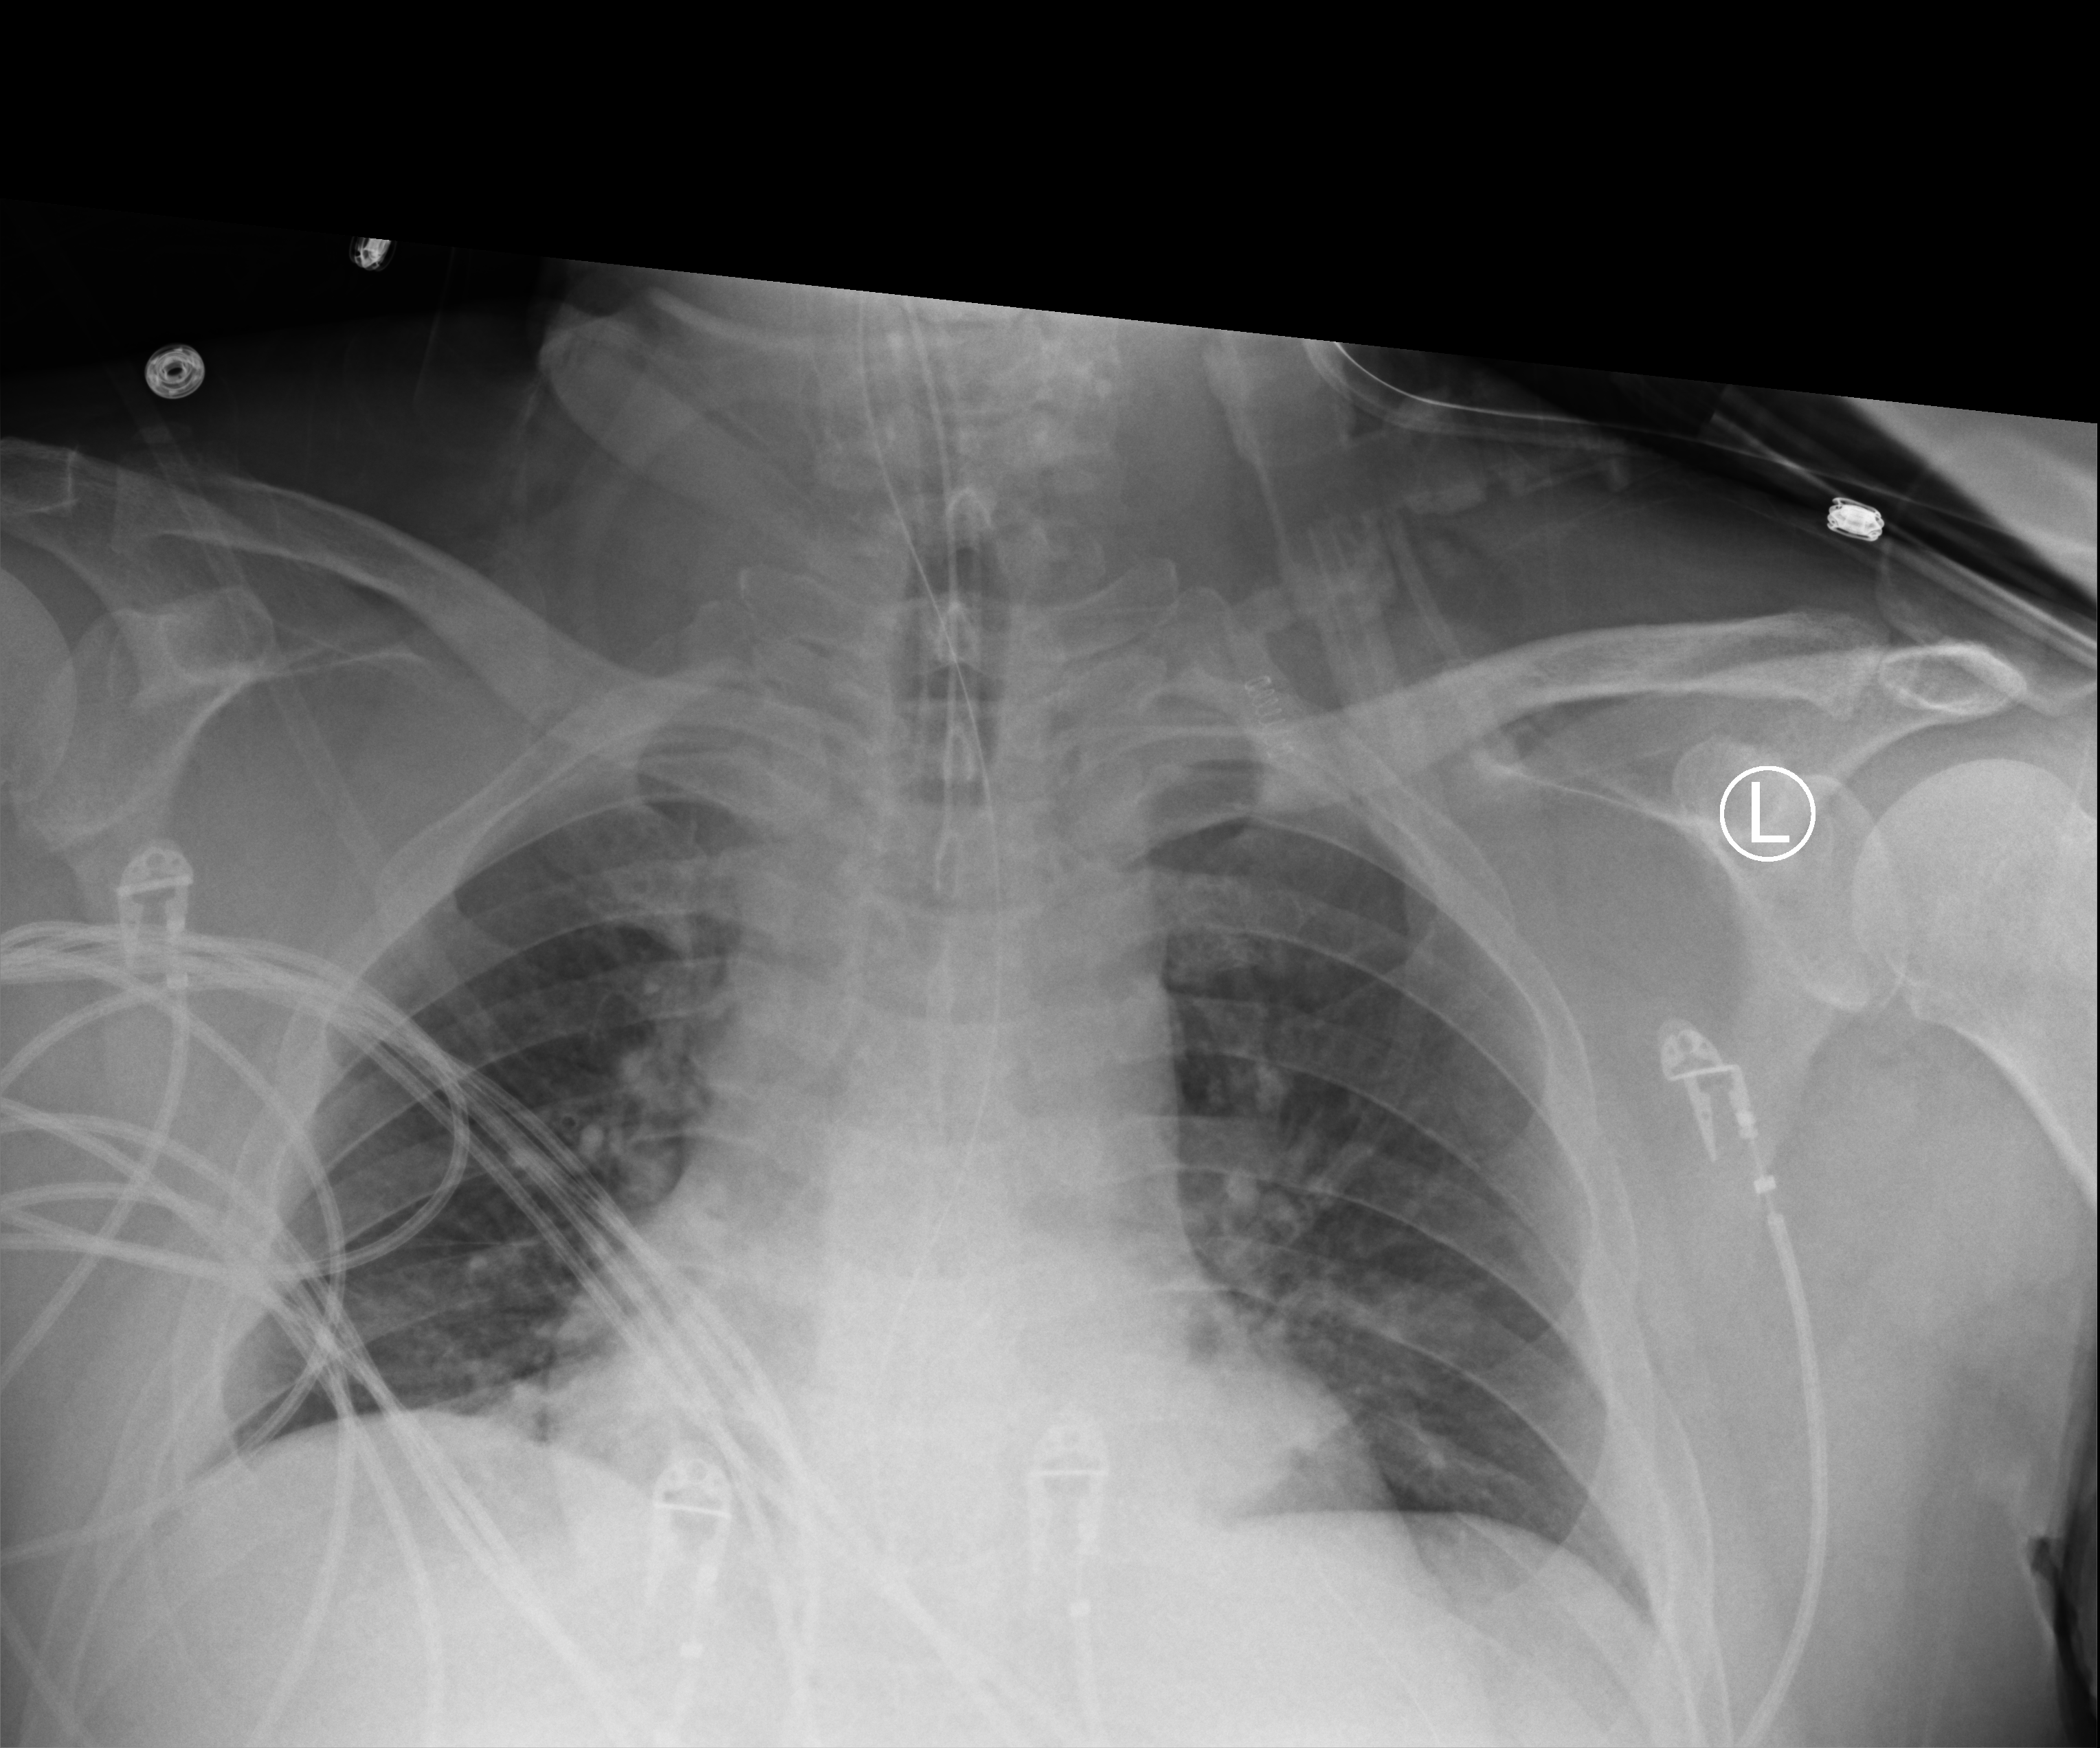
Portable chest radiograph. Male patient hospitalised with COVID-19, age 18–59 years.
From the hospital-stay record, not from the radiograph (when in the stay this image was taken is not recorded): mechanically ventilated during this hospital stay: yes; admitted to intensive care during this hospital stay: yes.